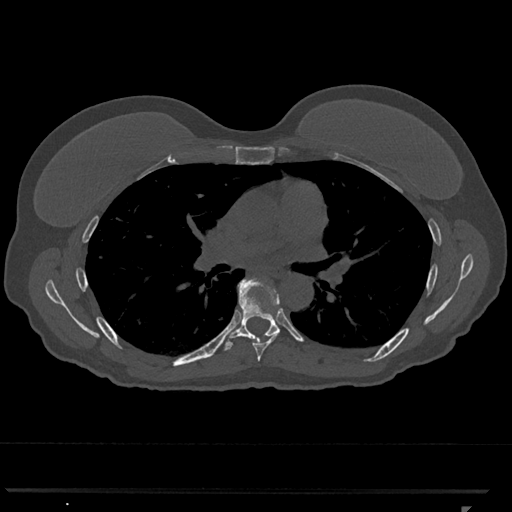
CT including the spine, one axial slice. Slice 737 of 793 in the series (ordered by position). Reconstruction kernel Br40s/3. Bone window (W 1800 / L 400 HU). 0.5 mm slice thickness. 512 × 512 image matrix. Patient: female, 62 years. Case-level facts recorded for this patient, not image findings: primary cancer: renal.
Annotated regions visible in this slice (semi-automatically segmented with operator editing):
- T6 vertebra: box from (x=238, y=279) to (x=280, y=362) px
- T7 vertebra: (x=220, y=278)–(x=280, y=351)